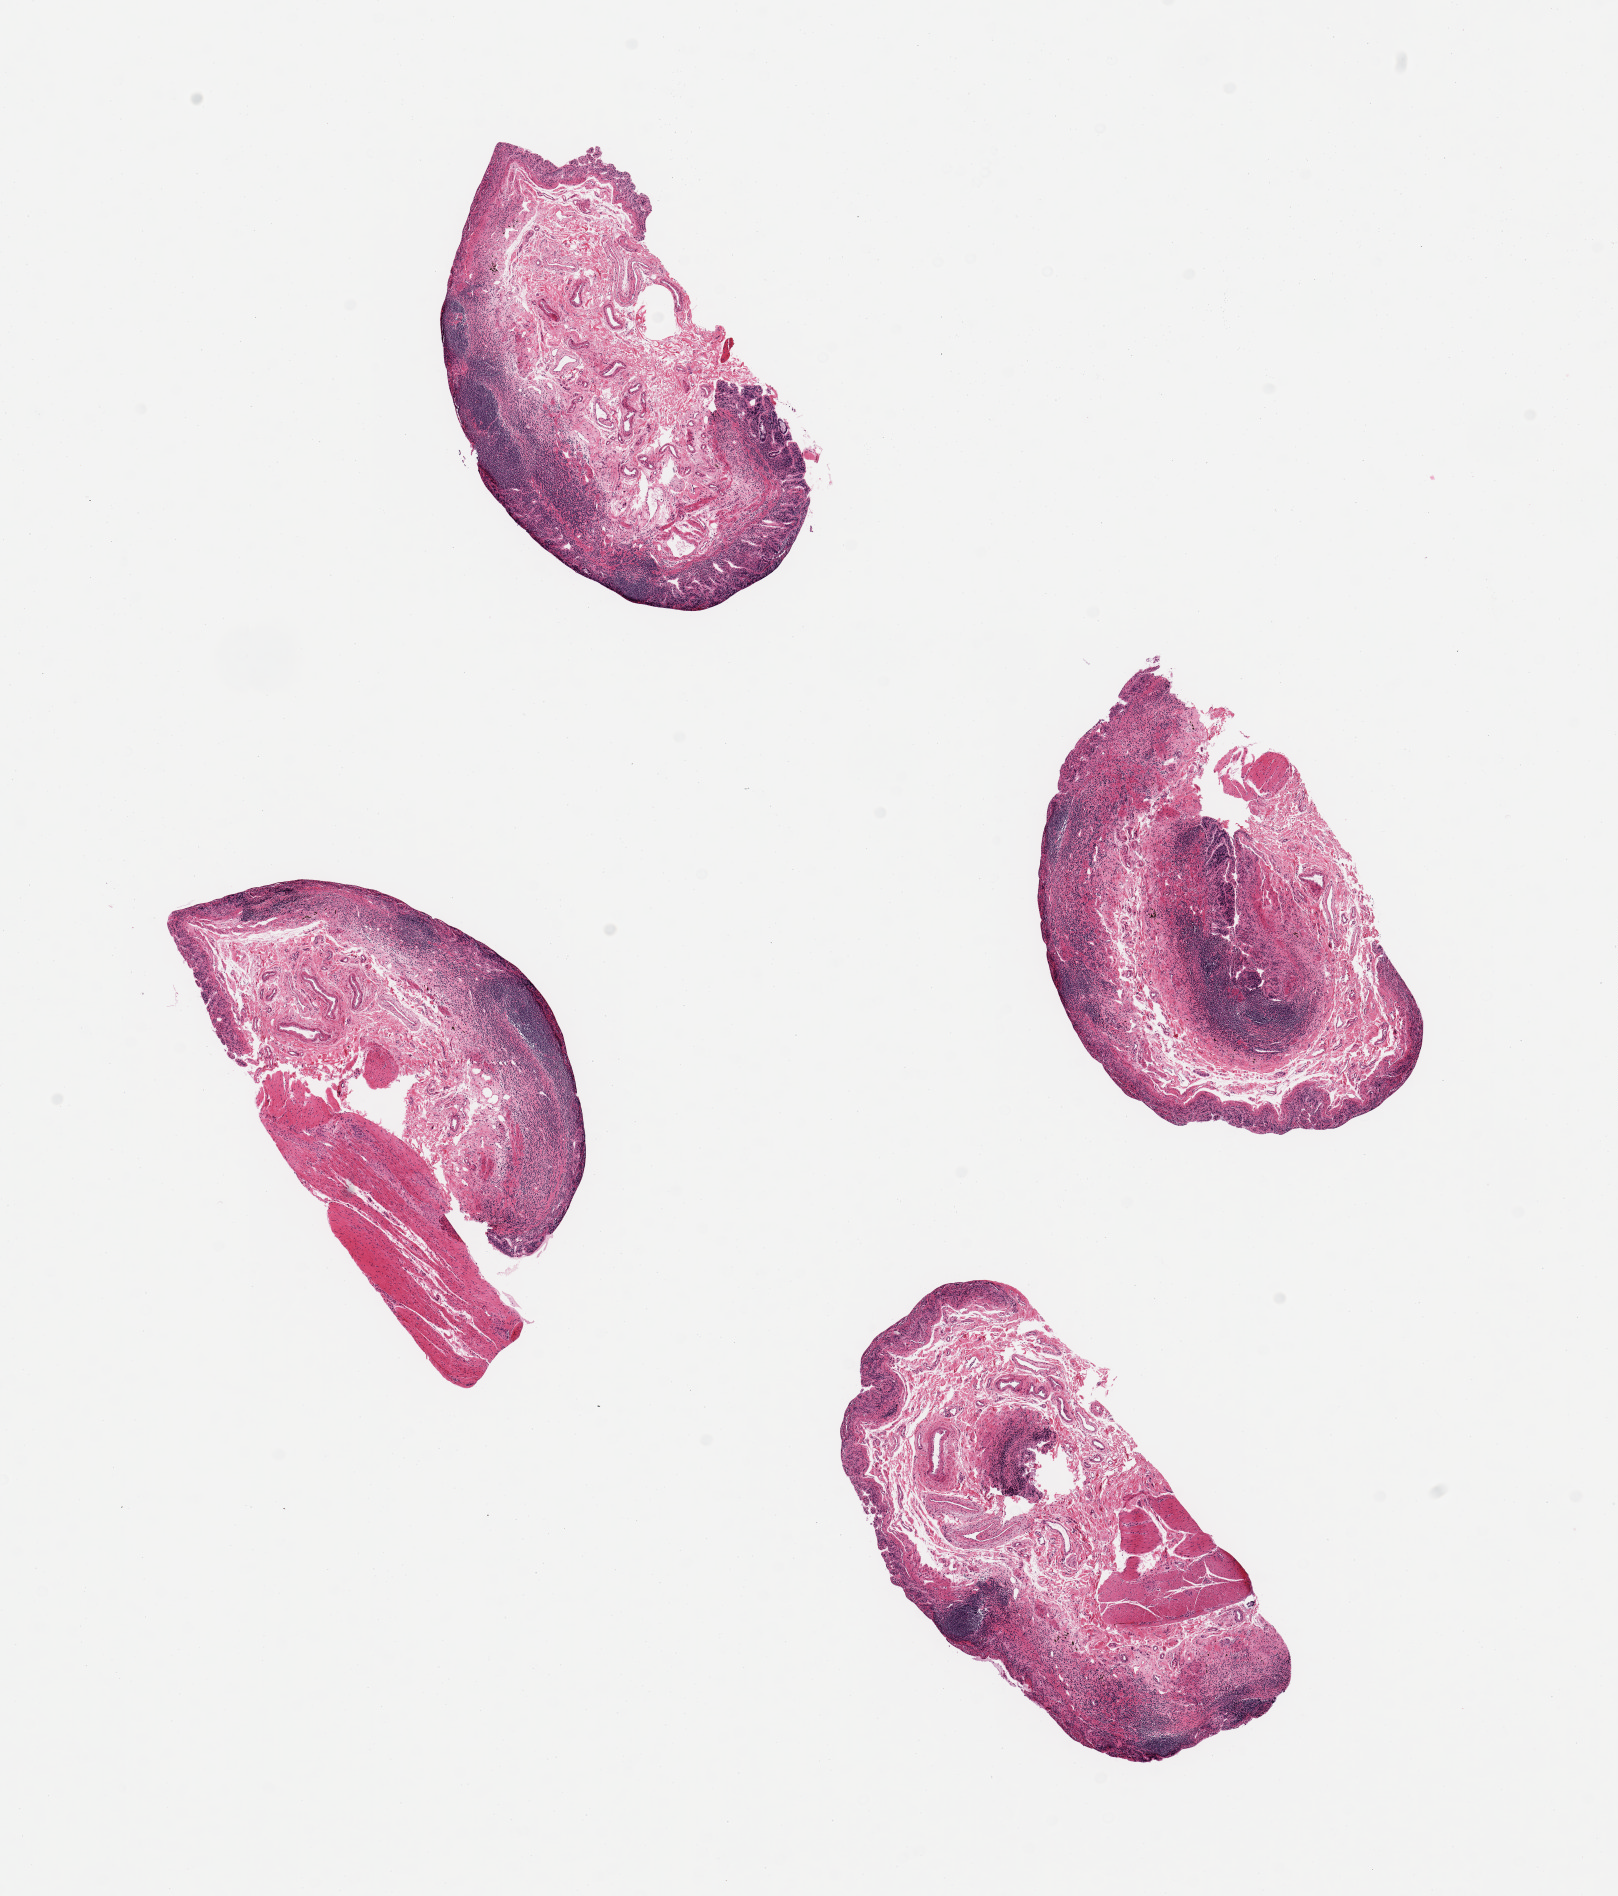
Digitized H&E-stained section — shown as a low-resolution overview of the whole scanned area (about 12.8 x 15.0 mm, from a 20x scan), PAXgene-fixed, paraffin-embedded tissue, target tissue: ileum, donor tissue sample. Donor: male.
Reviewer comment on this tissue sample: 4 pieces. target lymphoid aggregates are ~40% of tissue.